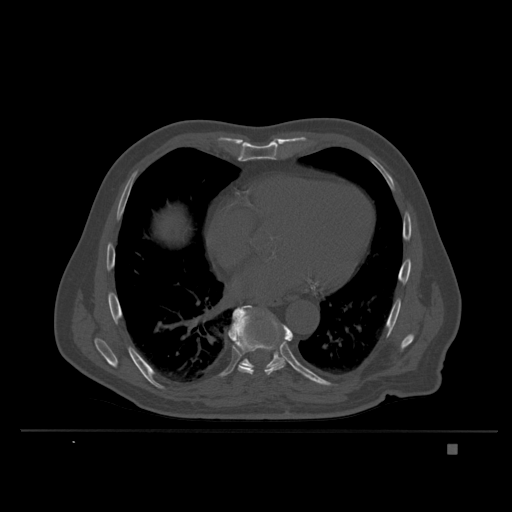
CT including the spine, one axial slice; position 223 of 435 along the scan axis; bone window (W 1800 / L 400 HU); 1.5 mm slice thickness; 512 × 512 image matrix, field of view 434 × 434 mm. Patient: male, 73 years. From the clinical record (not read from this slice): primary cancer: skin.
Annotated regions visible in this slice (semi-automatic segmentation, software-assisted and operator-edited):
- T6 vertebra: bounding box (x1, y1, x2, y2) in pixels: (278, 336, 288, 354)
- T8 vertebra: (228, 310, 294, 376)
- T9 vertebra: (232, 305, 306, 376)